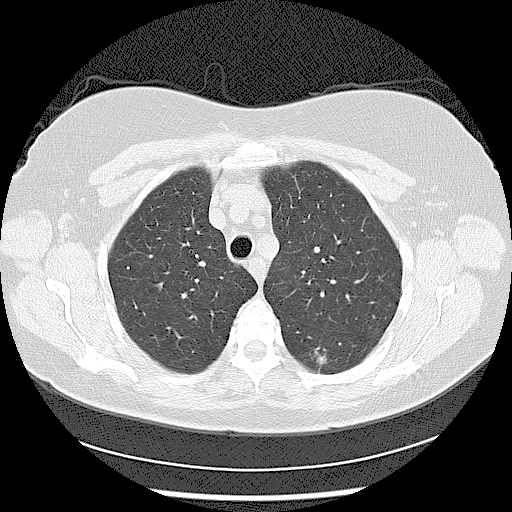
Low-dose screening chest CT, axial slice. Baseline annual screen. Lung window (W 1500 / L -600 HU). 2.5 mm slice thickness. Lung (sharp) reconstruction kernel (LUNG). Slice 26 of 116 in the series. 512 × 512 image matrix. Female participant, aged 56 years at enrolment. Current smoker at enrolment.
Expert reader's lesion annotation, bounding box <295,334,345,384> (left, top, right, bottom; pixels). The screening reader recorded 2 non-calcified nodules or masses ≥4 mm on this exam (left lower lobe, left lower lobe); which of them this box marks is not recorded. Official screen result: positive, change unspecified: nodule(s) >= 4 mm or enlarging nodule(s), mass(es), or other non-specific abnormalities suspicious for lung cancer. Participant outcome: lung cancer diagnosed 638 days after this screen — adenocarcinoma, NOS, left lower lobe, moderately differentiated (G2), stage IIA (AJCC 6th edition), 15 mm at pathology.